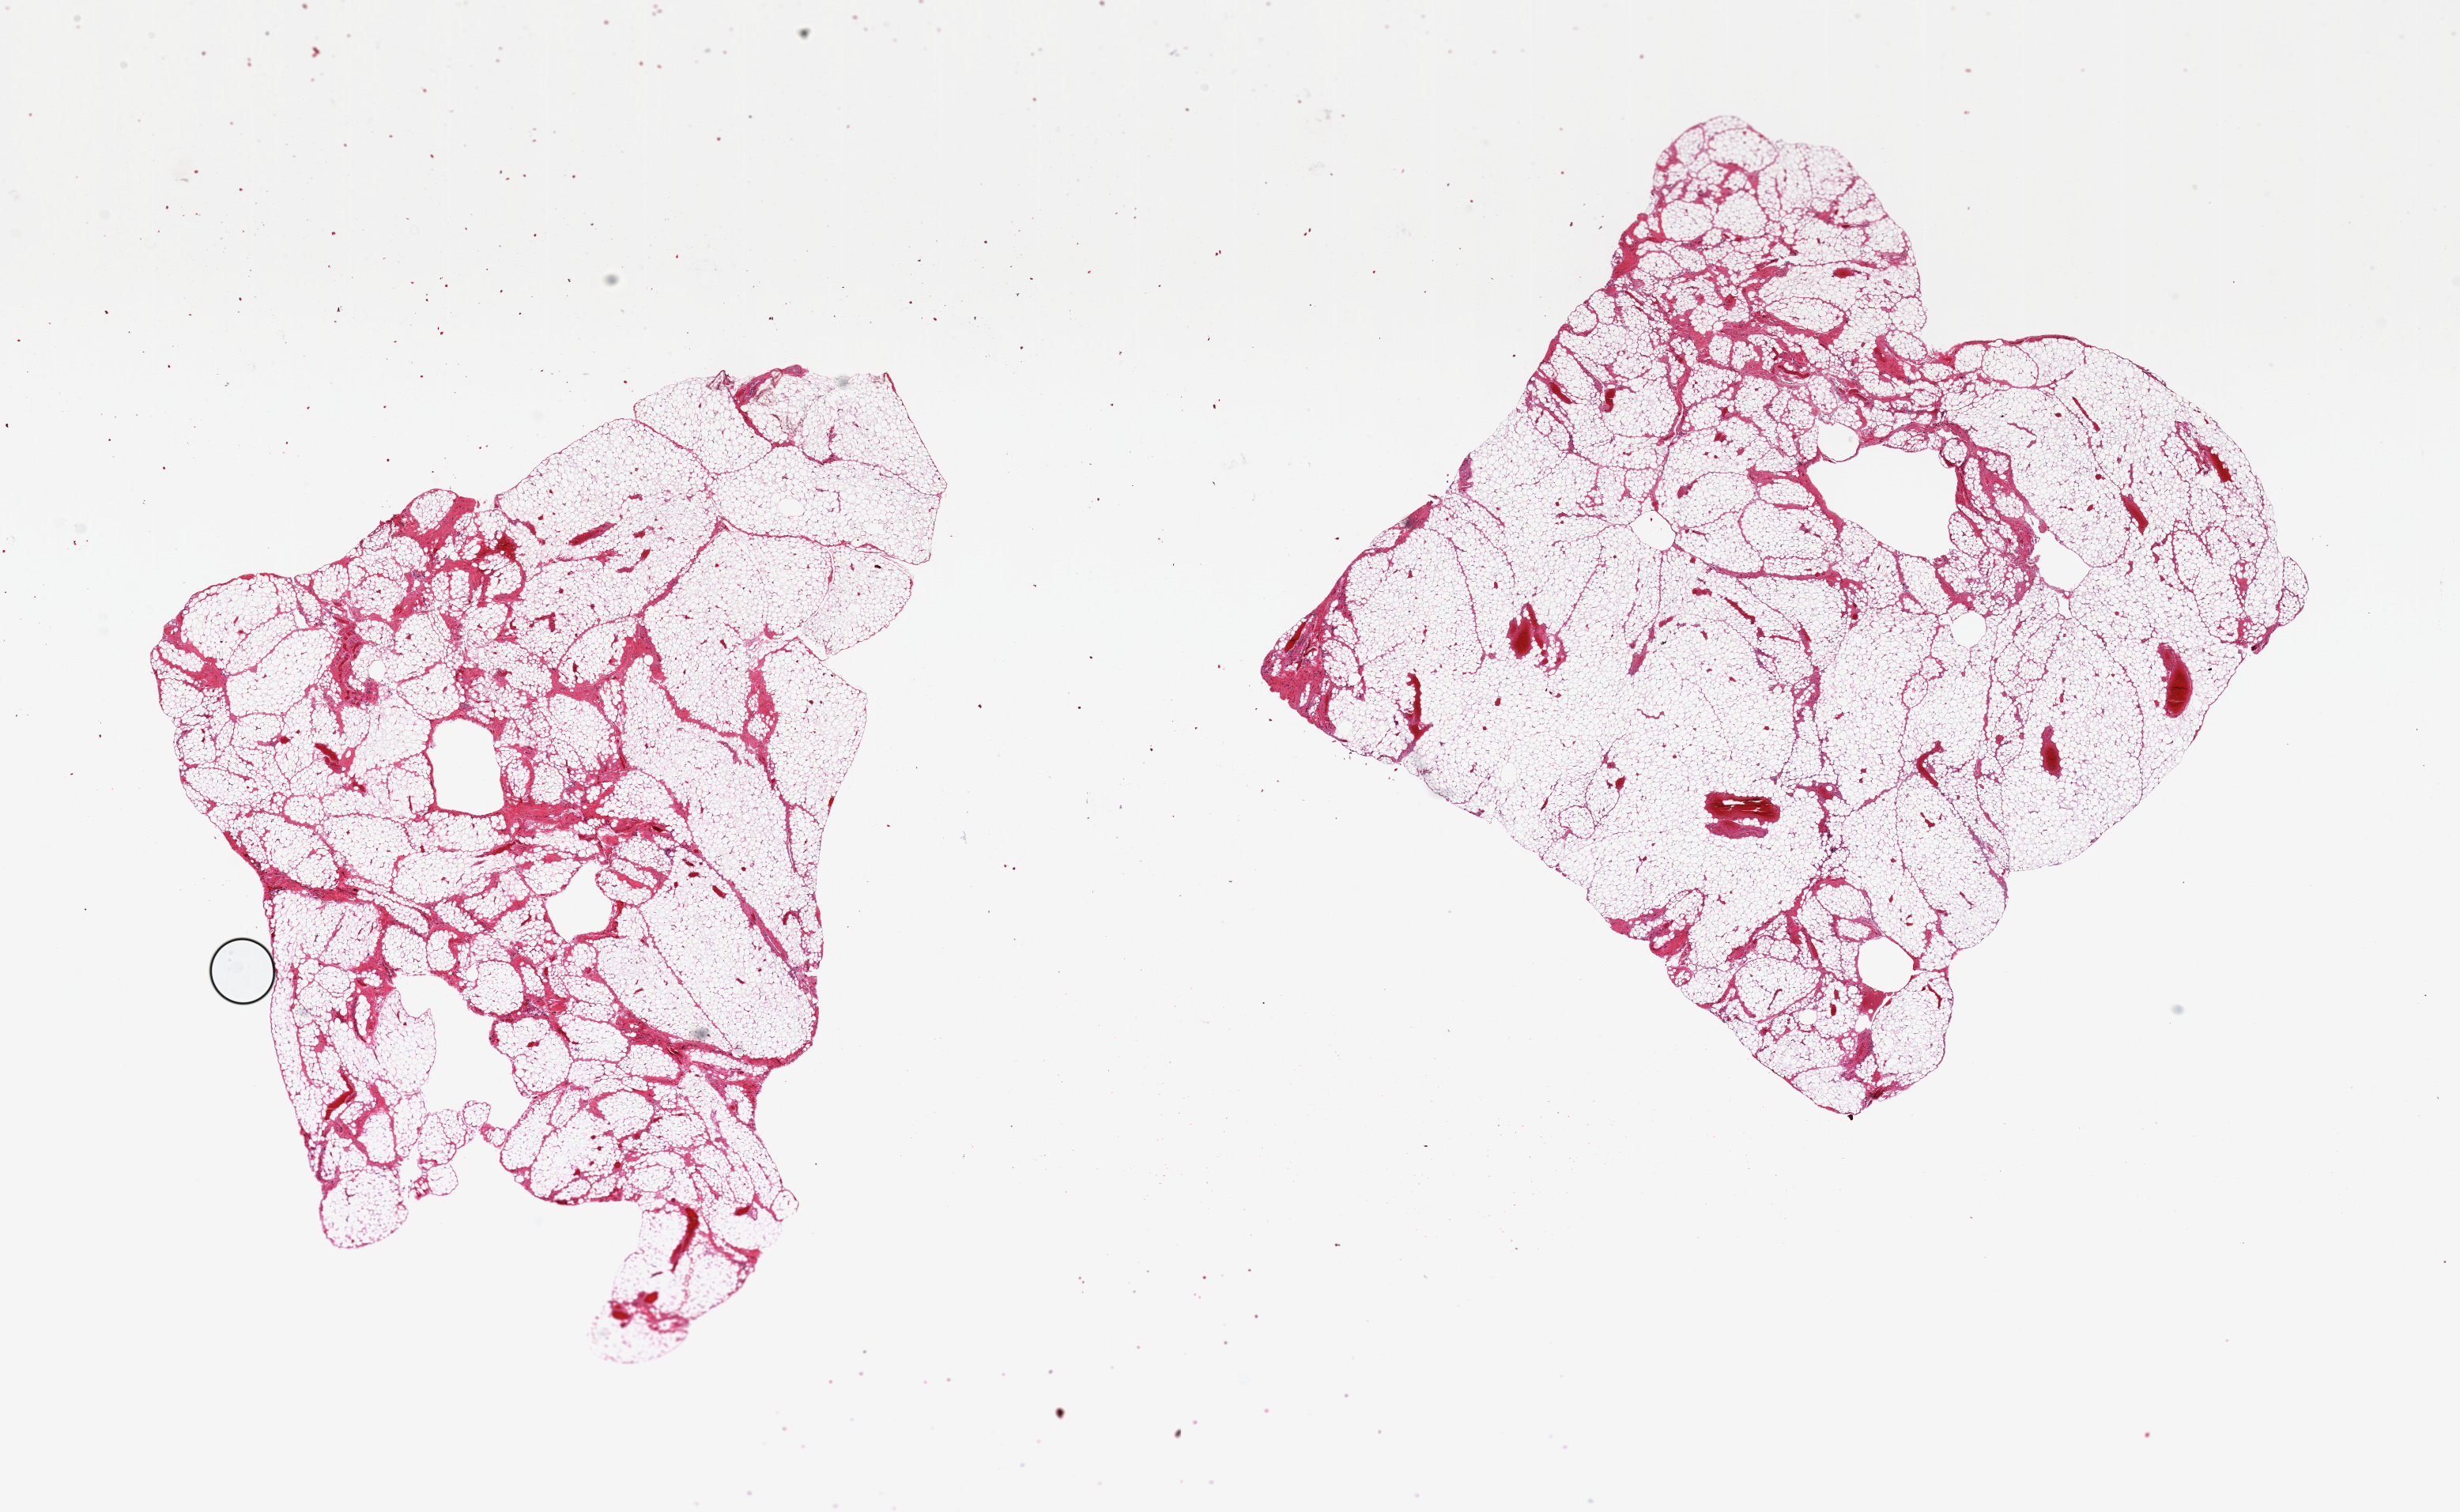
Haematoxylin and eosin whole-slide image, low-resolution overview of the scanned area, about 24.6 x 15.1 mm (slide scanned at 20x). PAXgene-fixed, paraffin-embedded tissue. Target tissue: omentum. Tissue donor sample. Donor sex: female.
Reviewer comment on this tissue sample: 2 pieces ~8x8mm.